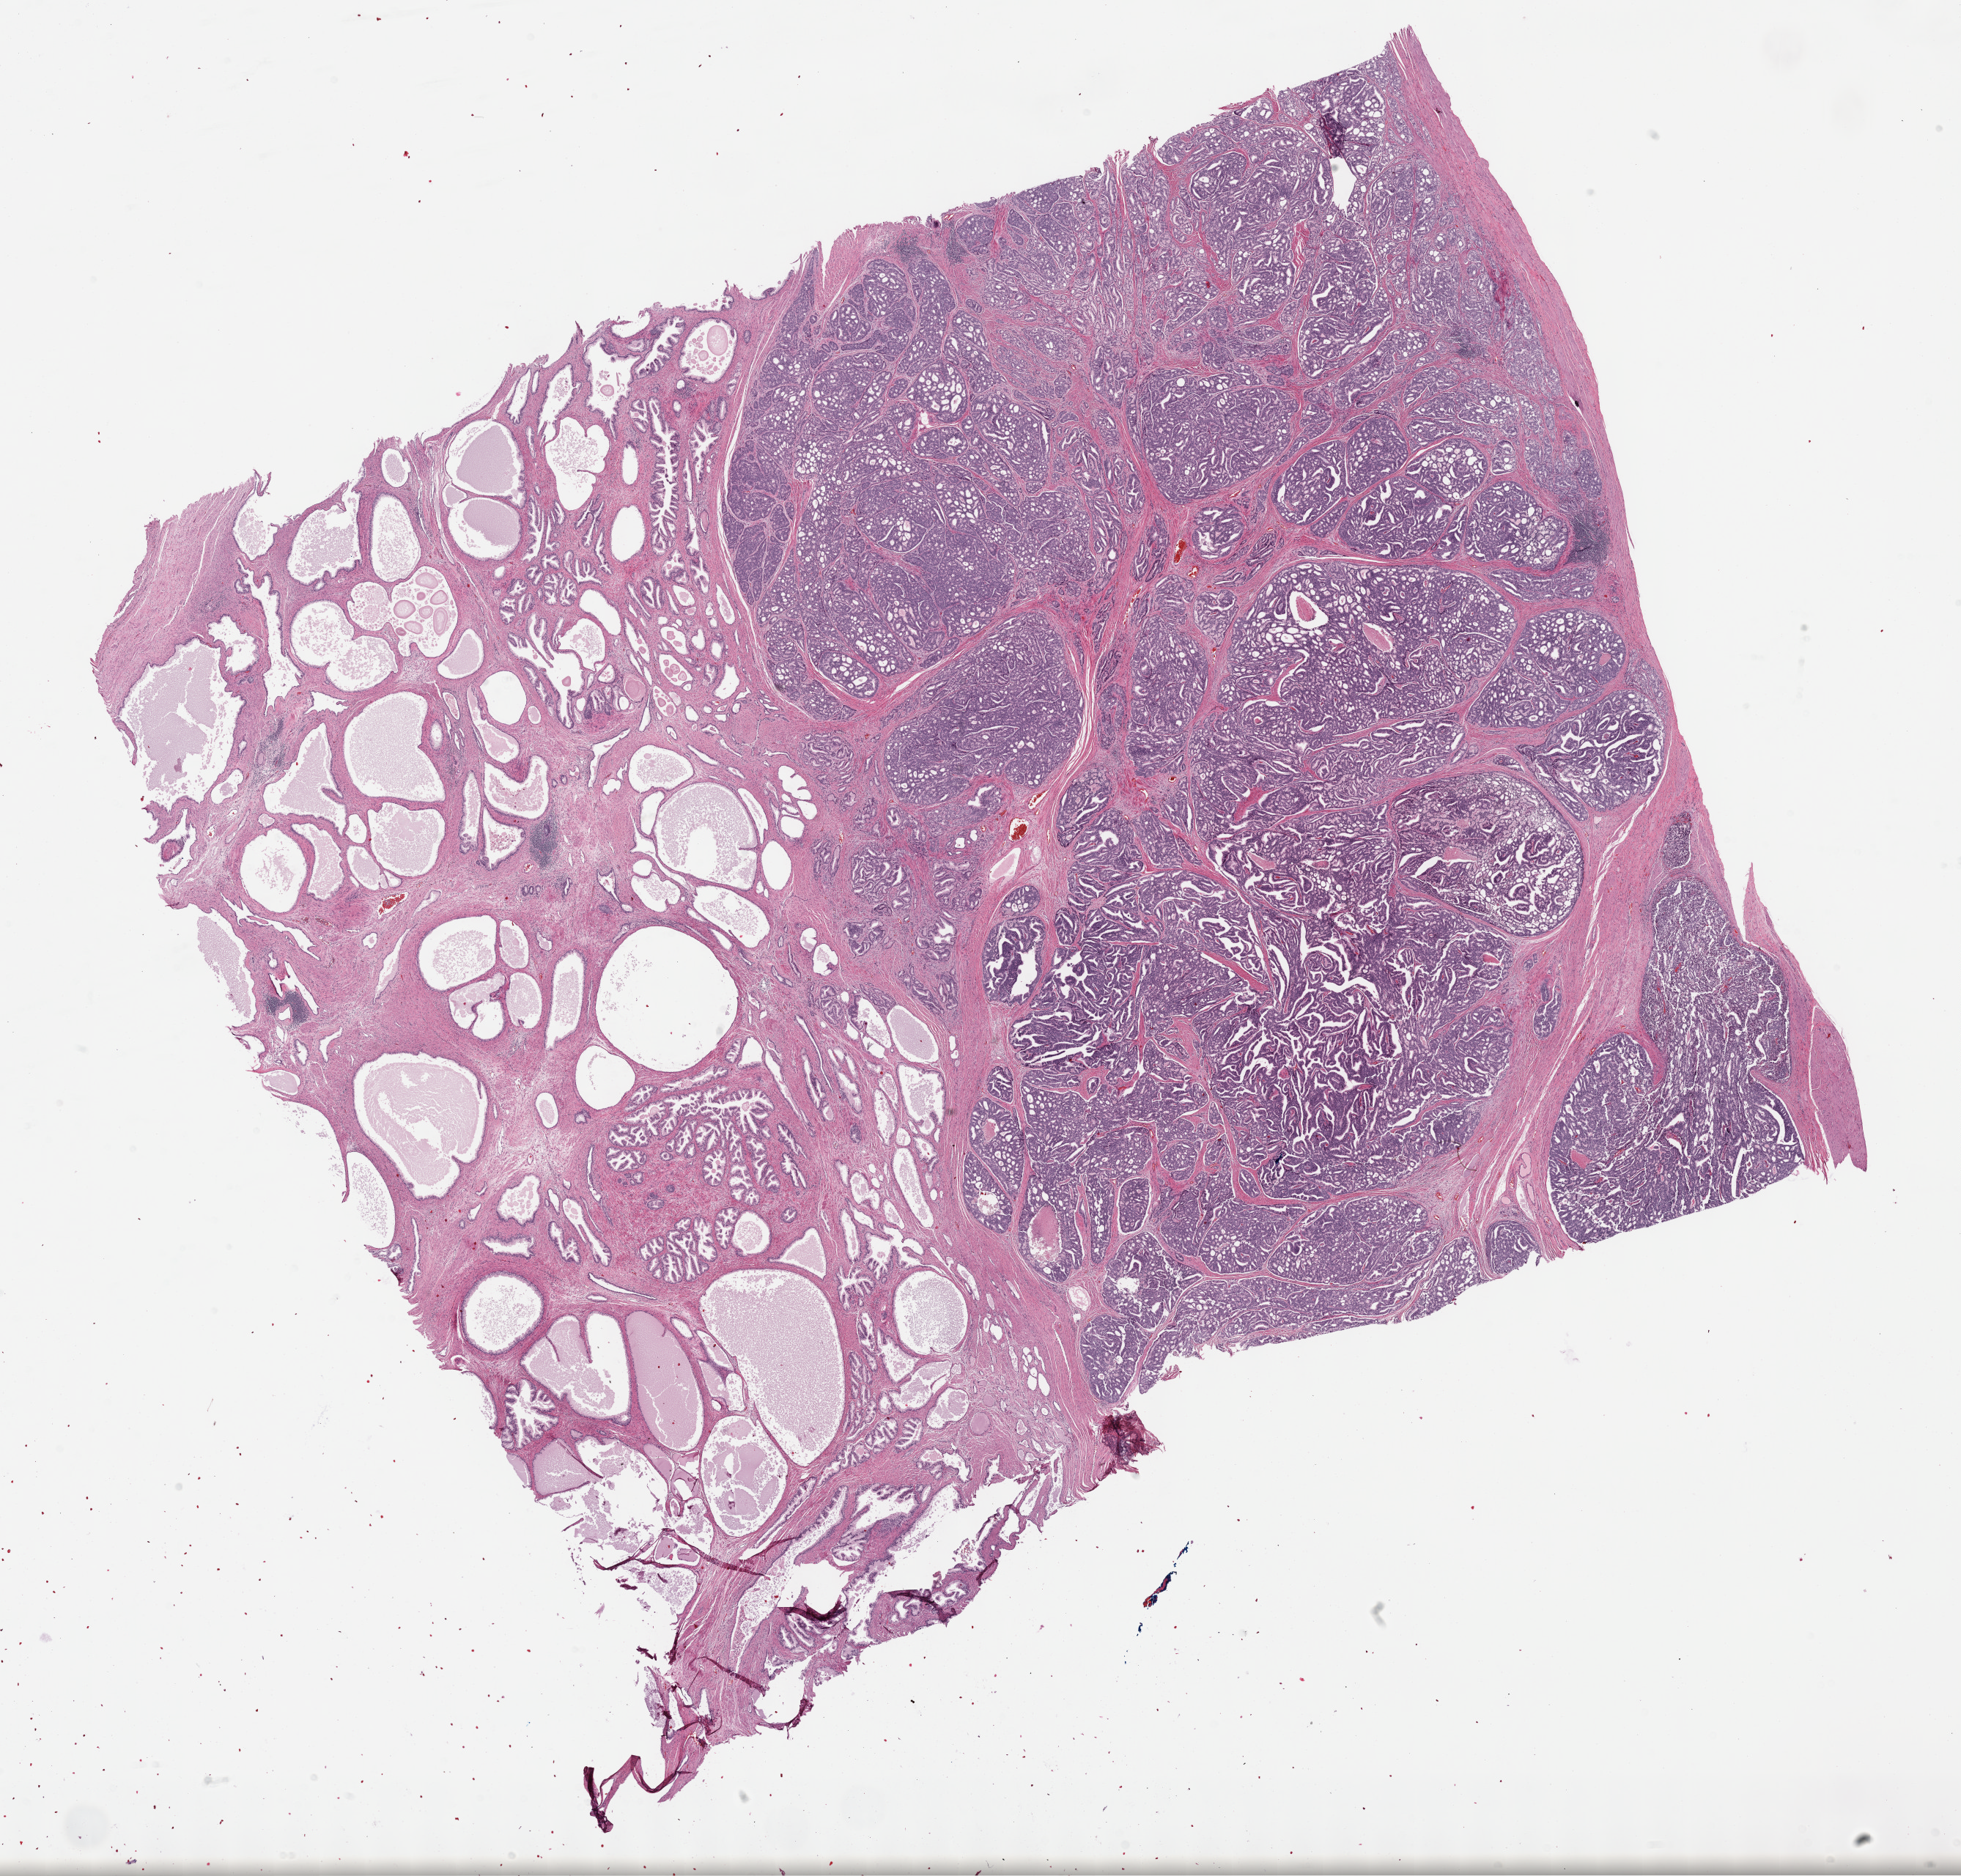
Whole-slide histology image, H&E, shown as a low-resolution overview of the whole scanned area (about 21.6 x 20.7 mm, from a 40x scan); formalin-fixed paraffin-embedded (FFPE) diagnostic section; sample: primary tumour, prostate. Patient: male, age at initial diagnosis 70 years. Gleason score: 8 (4+4).
Histologic diagnosis: Adenocarcinoma, NOS (prostate gland). Lymph nodes positive (case pathology): 0 of 16 examined.